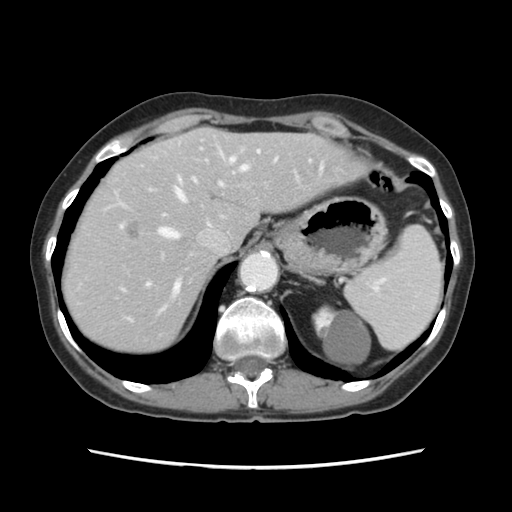
Contrast-enhanced abdominal CT, one axial slice; position 92 of 120 along the scan axis; 120 kVp; intravenous contrast given; soft-tissue window (W 400 / L 40 HU); 2.5 mm slice thickness; 512 × 512 image matrix, field of view 330 × 330 mm. Female patient, age 70 years. Case-level facts recorded for this patient, not image findings: diagnosis: colorectal cancer liver metastases, imaged before liver resection; multiple liver metastases: no; largest metastasis: 2.5 cm; disease in both lobes: no.
Structures marked on this image (manually delineated by an expert):
- hepatic veins: box from (x=159, y=157) to (x=248, y=313) px
- liver: (x=65, y=129)–(x=361, y=351)
- planned liver remnant (the part of the liver to remain after resection): (x=129, y=129)–(x=361, y=283)
- portal vein (with intrahepatic branches): (x=120, y=150)–(x=260, y=286)
- liver metastasis: (x=128, y=223)–(x=140, y=238)